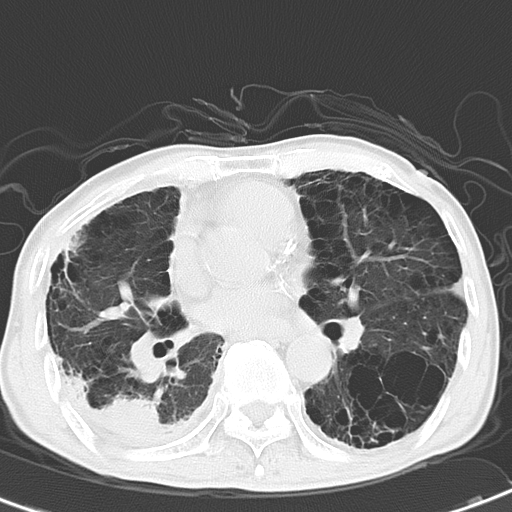
Chest CT, one axial slice; slice 23 of 51 in the series (ordered by position); lung window (W 1500 / L -600 HU); 6 mm slice thickness; 512 × 512 image matrix. Patient: male, 67 years. From the clinical record (not read from this slice): clinical TNM (as recorded): T2 N3 M1.
Annotated regions visible in this slice (bounding box drawn by a radiologist):
- lung tumour (recorded histology: adenocarcinoma): box from (x=98, y=394) to (x=166, y=447) px